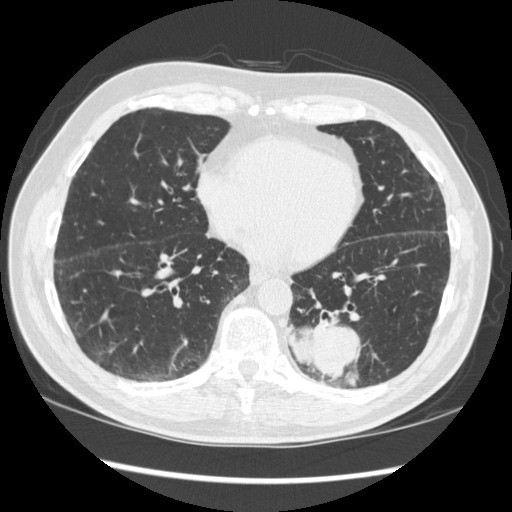
Low-dose screening chest CT, one axial slice. Slice 121 of 348 in the series (ordered by position). Reconstruction kernel STANDARD. Lung window (W 1500 / L -600 HU). 512 × 512 image matrix, field of view 360 × 360 mm.
Structures marked on this image (expert manual segmentation):
- lesion 1 (tumor, lower lobe of left lung): bounding box (x1, y1, x2, y2) in pixels: (289, 317, 360, 381)